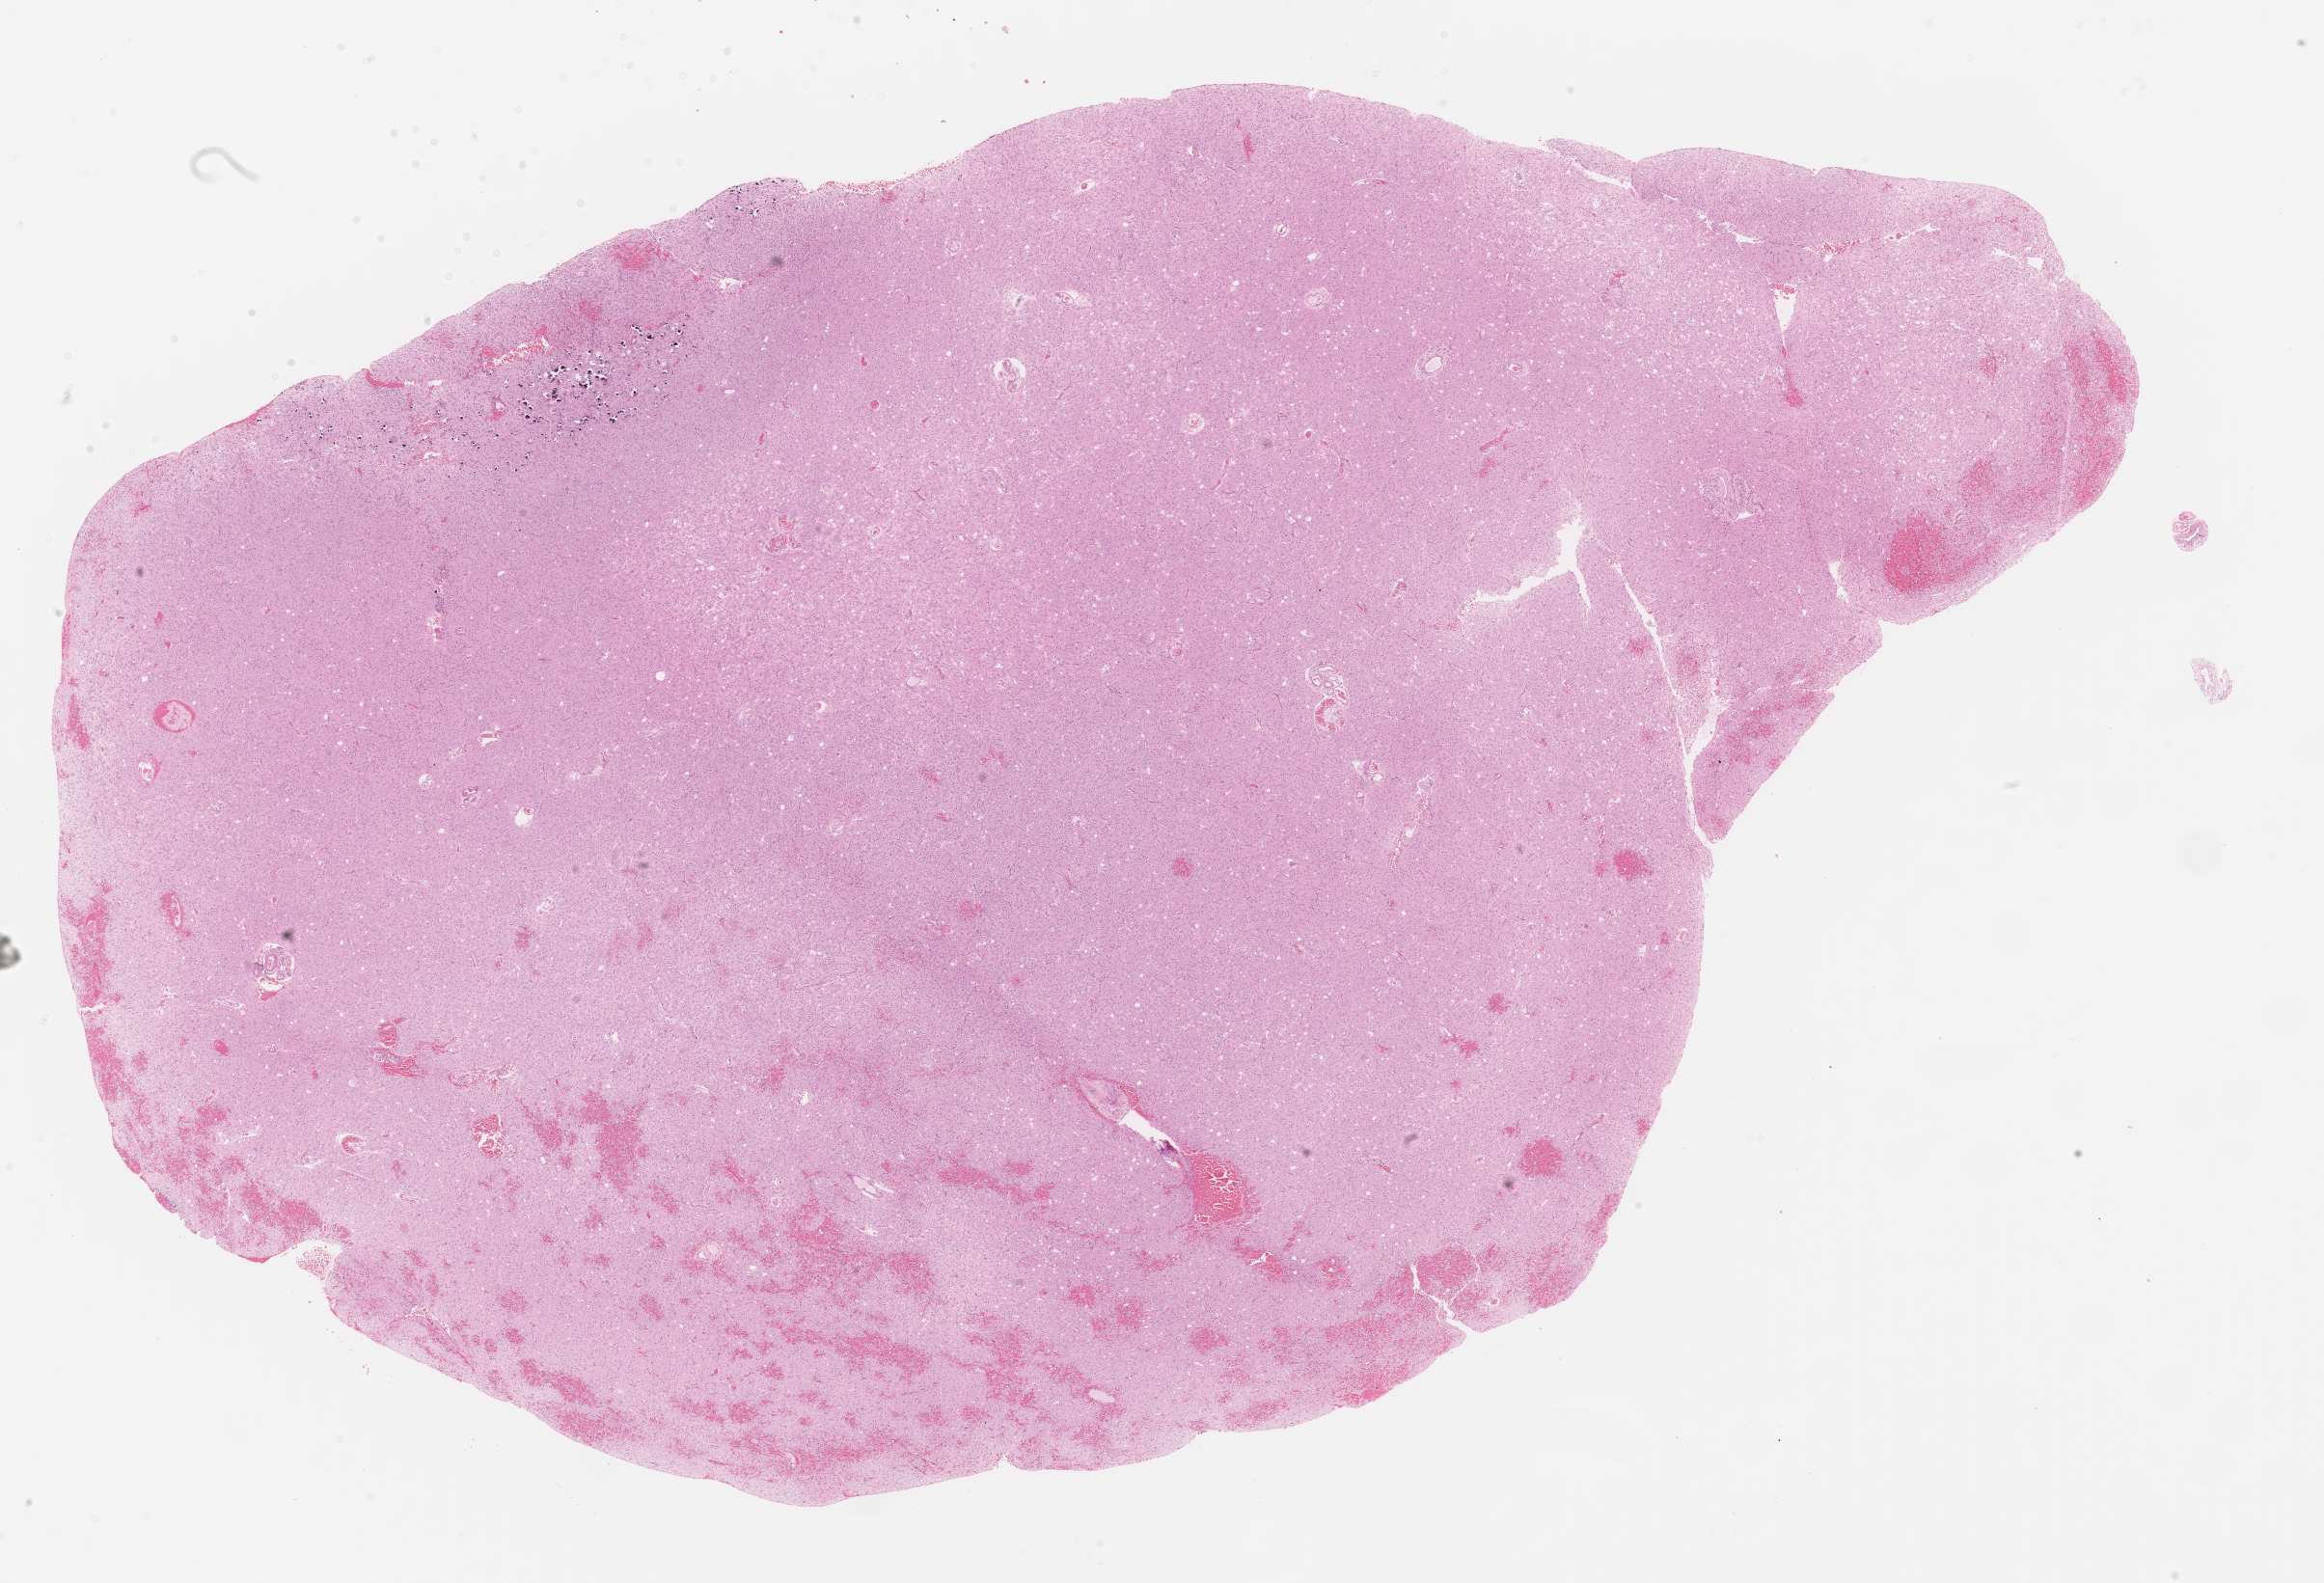
Whole-slide histology image, Hematoxylin and eosin (H&E) stained, a low-resolution overview of the entire scanned area, about 19.4 x 13.2 mm (slide scanned at 40x). Formalin-fixed paraffin-embedded (FFPE) diagnostic section. Sample: primary tumour, brain. Patient: male, age at initial diagnosis 52 years. Histologic grade: G3 (poorly differentiated).
Pathologic diagnosis: Oligodendroglioma, anaplastic. Laterality: left.